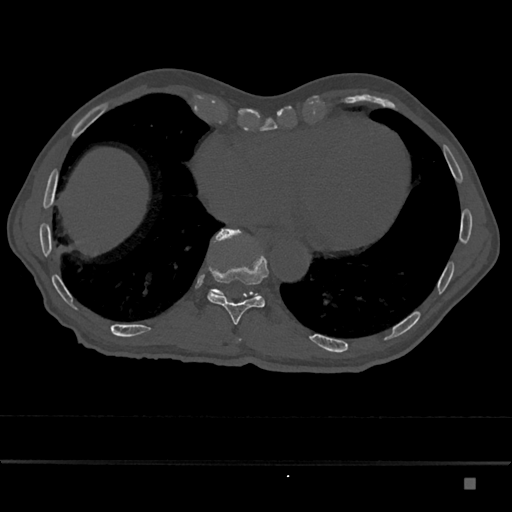
CT including the spine, one axial slice; slice 731 of 797 in the series (ordered by position); bone window (W 1800 / L 400 HU); 0.5 mm slice thickness; 512 × 512 image matrix. Male patient, age 72 years. From the clinical record (not read from this slice): primary cancer: prostate.
Outlined on this slice (semi-automatic segmentation, software-assisted and operator-edited):
- T10 vertebra: bounding box [x1, y1, x2, y2] px = [207, 236, 269, 325]
- T11 vertebra: [209, 229, 258, 297]